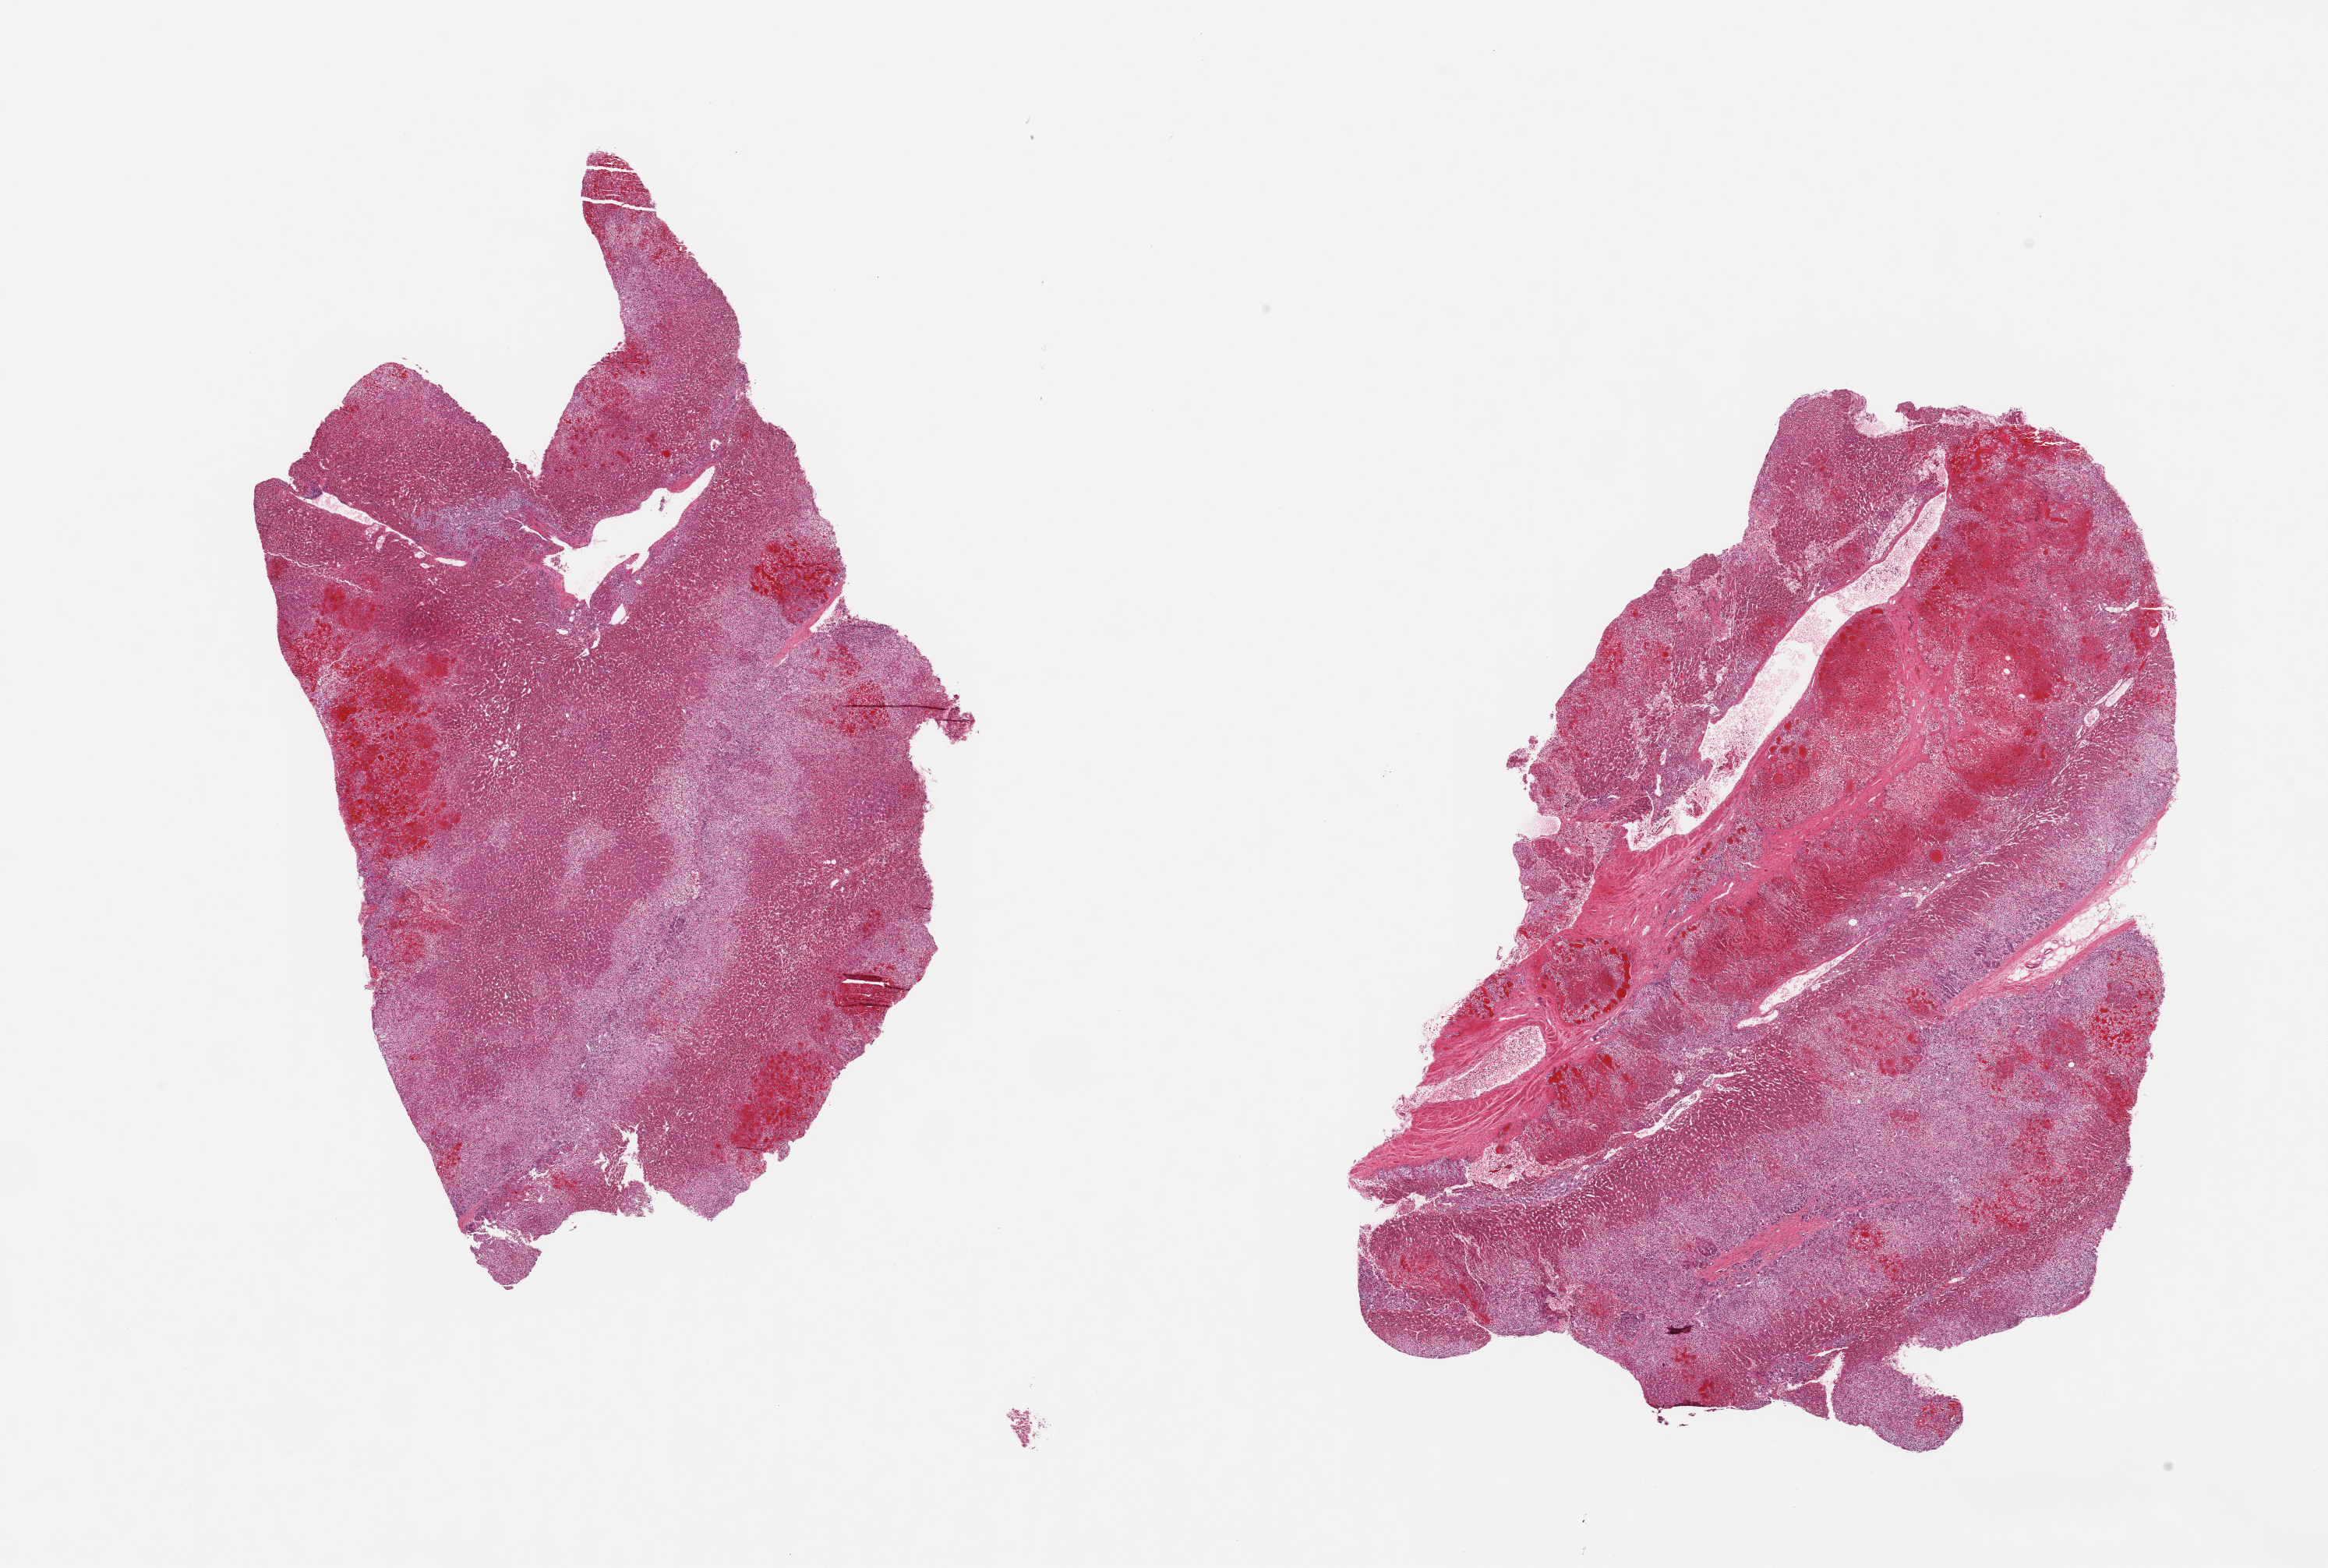
Hematoxylin and eosin (H&E) whole-slide image, a low-resolution overview of the entire scanned area, about 23.6 x 15.9 mm, PAXgene-fixed, paraffin-embedded tissue, sampled site (target tissue): adrenal gland, donor tissue sample. Donor: male.
* review note (as recorded): 2 pieces; moderately congested; well dissected; no fat